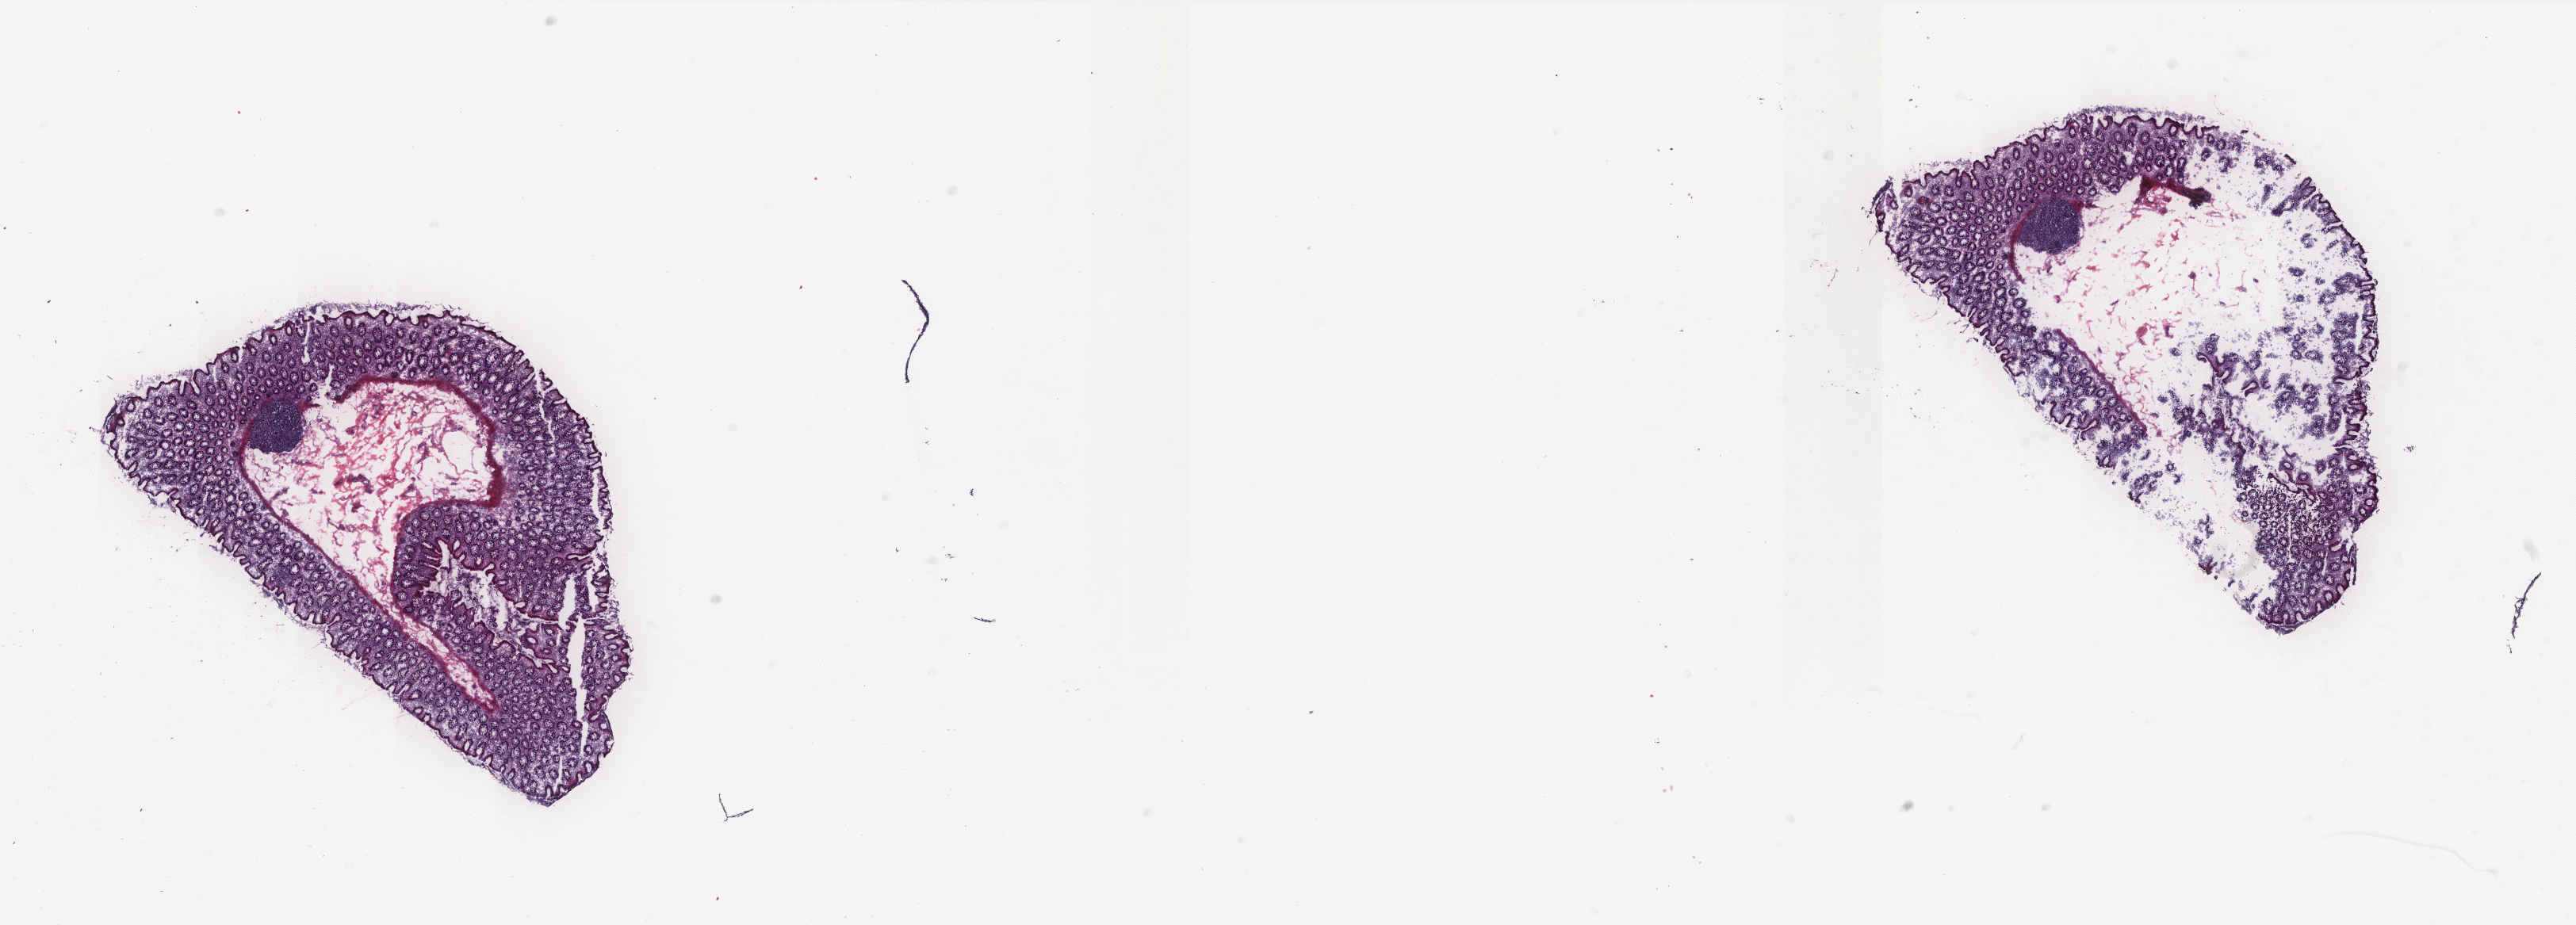
Digitized Hematoxylin and eosin (H&E) stained tissue section (whole slide), a low-resolution overview of the entire scanned area, about 25.9 x 9.3 mm. Frozen section. Colon, solid tissue normal (non-tumour tissue) sample. Patient: male, age at initial diagnosis 47 years. Pathologist review of this section (percent, as recorded): tumour cells 0%, normal cells 100%. Inflammatory infiltration, as recorded: lymphocyte infiltration 45%, monocyte infiltration 10%, neutrophil infiltration 0%.
* this section: solid tissue normal (non-tumour) sample from the same patient
* patient diagnosis: Mucinous adenocarcinoma (ascending colon)